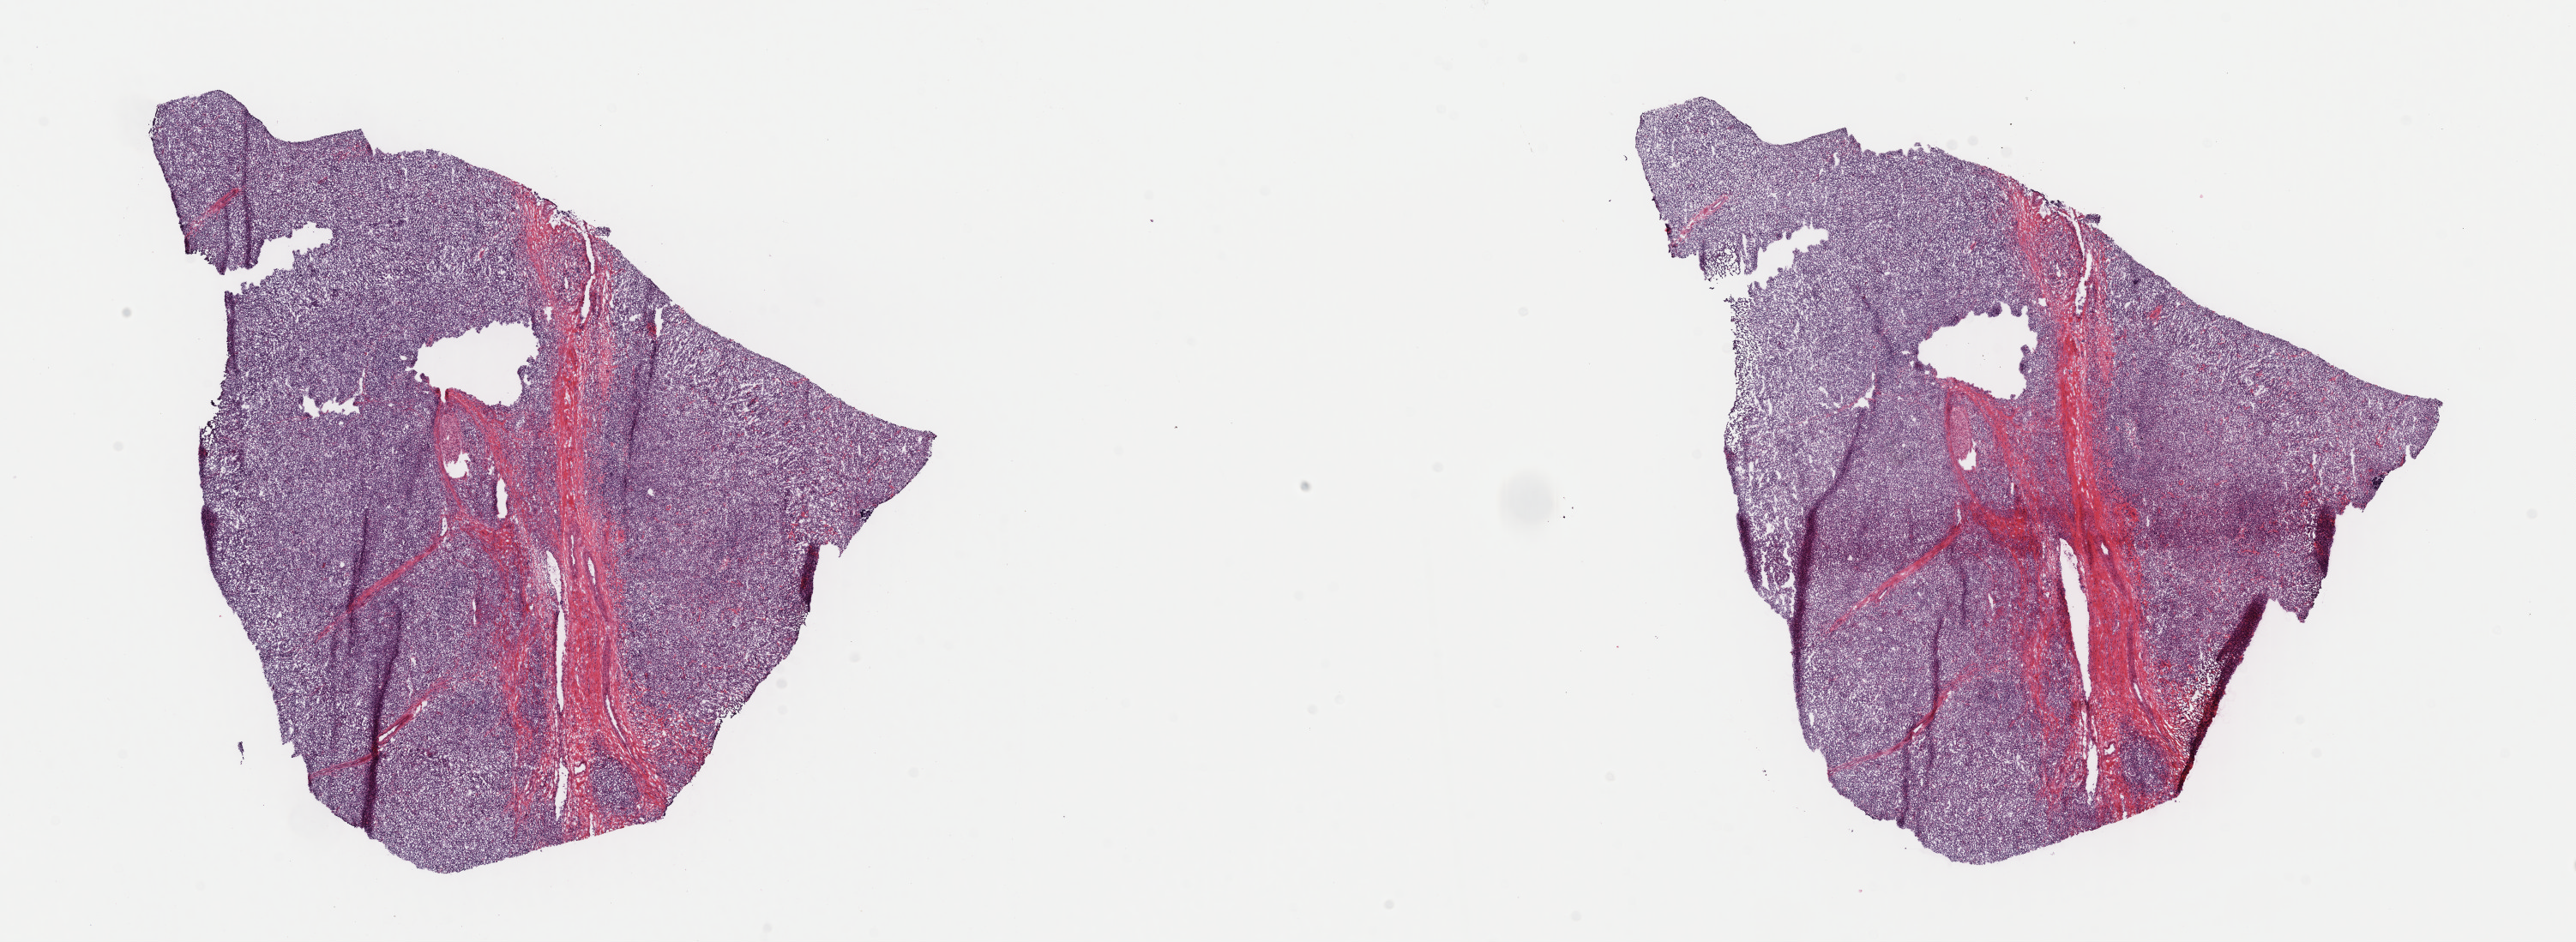
Digitized H&E-stained tissue section (whole slide) — whole scanned area (about 23.7 x 8.7 mm, acquisition: 40x scan) shown as a low-resolution overview. Frozen section from the top of the tissue portion. Lymphoid tissue, primary tumour sample. Male, age 73 years at initial diagnosis. Slide review estimates, as recorded: tumour cells 90%, tumour nuclei 80%, normal cells 0%, stromal cells 10%, necrosis 0%. Infiltration values recorded for this section: lymphocyte infiltration 80%, monocyte infiltration 10%, neutrophil infiltration 5%.
• pathologic diagnosis: Diffuse large B-cell lymphoma, NOS (lymph nodes of head, face and neck)